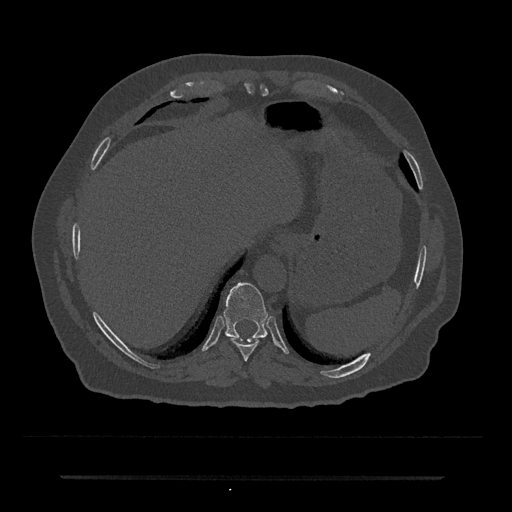
CT including the spine, one axial slice; position 251 of 797 along the scan axis; 120 kVp; bone window (W 1800 / L 400 HU); 512 × 512 image matrix, field of view 437 × 437 mm. Male patient, age 69 years. From the clinical record (not read from this slice): primary cancer: prostate.
Structures marked on this image (semi-automatically segmented with operator editing):
- T10 vertebra: bounding box [x1, y1, x2, y2] px = [223, 282, 268, 342]
- T9 vertebra: [231, 338, 259, 361]